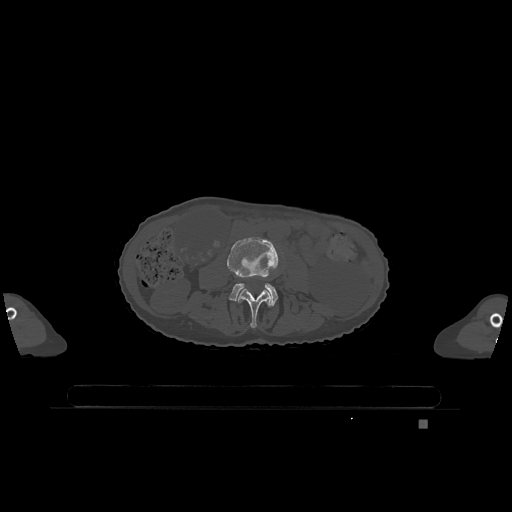
CT including the spine, one axial slice; position 330 of 1317 along the scan axis; bone window (W 1800 / L 400 HU); 0.5 mm slice thickness; 512 × 512 image matrix. Female patient, age 74 years. From the clinical record (not read from this slice): primary cancer: lung; vertebrae with lytic lesions (as recorded): T1, T4, T5, T6, L4, L5.
Structures marked on this image (semi-automatically segmented with operator editing):
- L3 vertebra: box from (x=238, y=288) to (x=272, y=328) px
- L4 vertebra: (x=227, y=236)–(x=278, y=305)